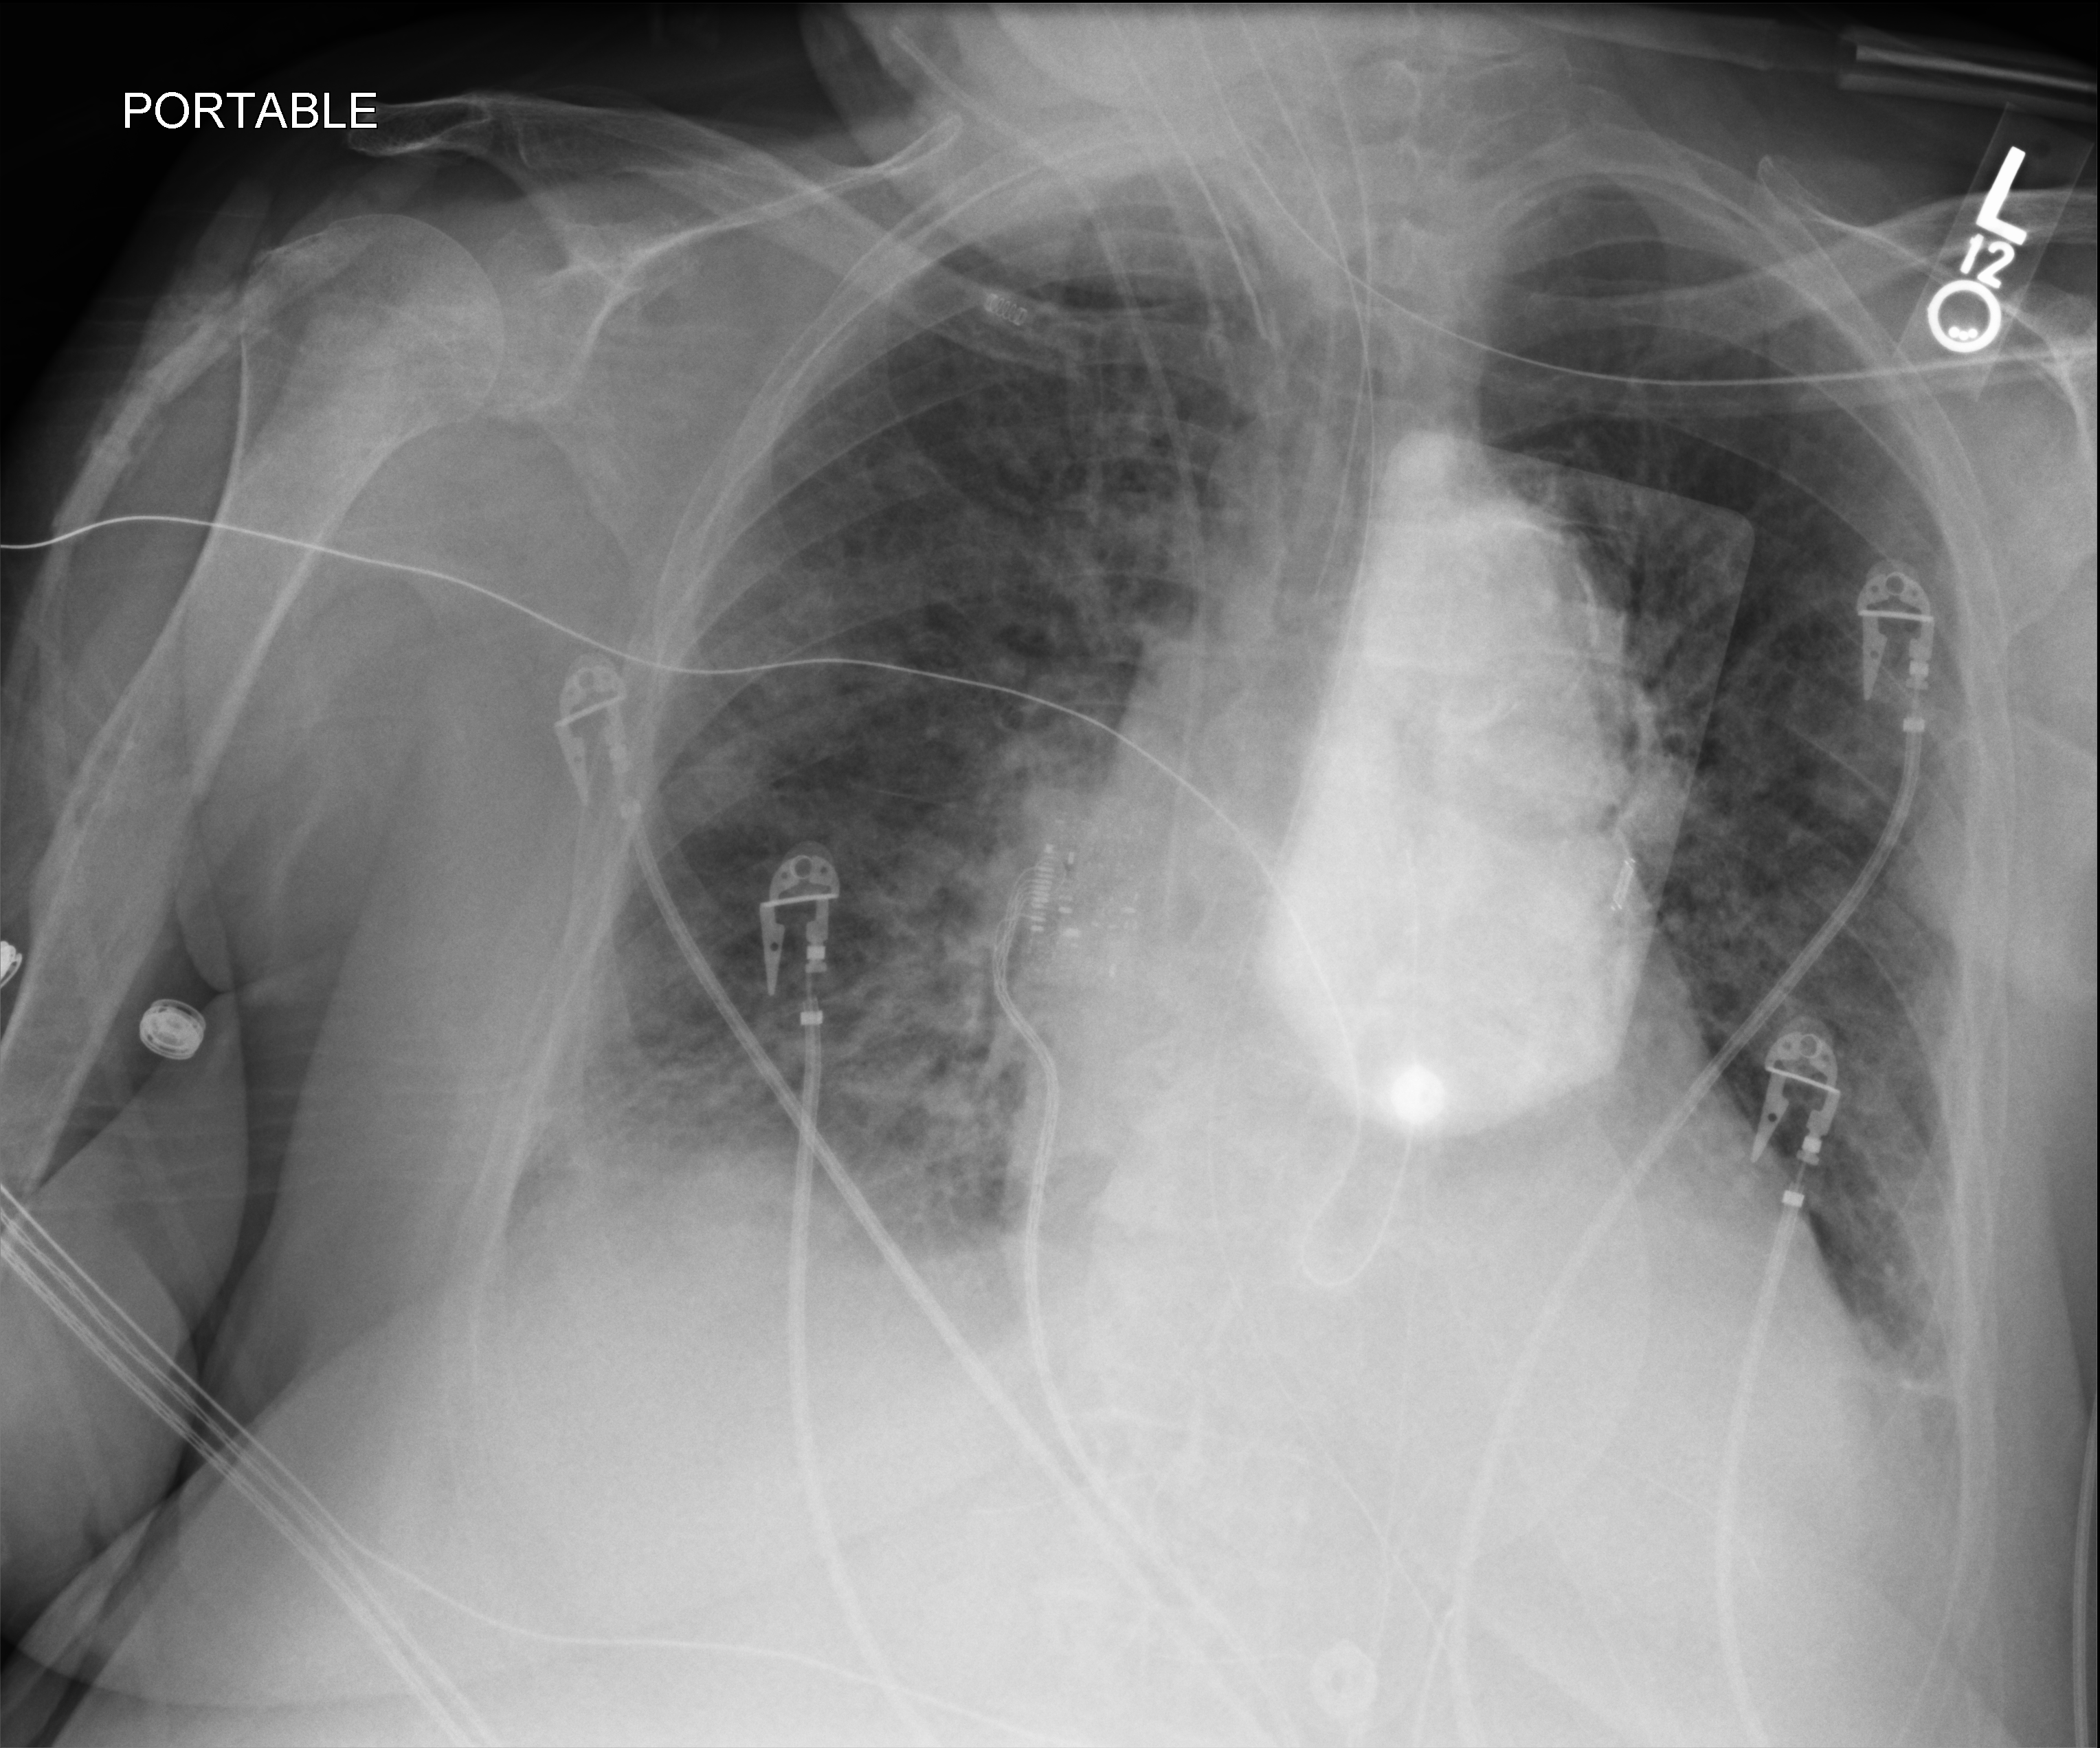
Chest X-ray (portable); anteroposterior (AP) projection. Female patient hospitalised with COVID-19, age 75–90 years.
Admission-level facts for this patient (not findings on this image; timing relative to this image not recorded): COPD (admission record): yes; admitted to intensive care during this hospital stay: yes; length of hospital stay: 10 days.